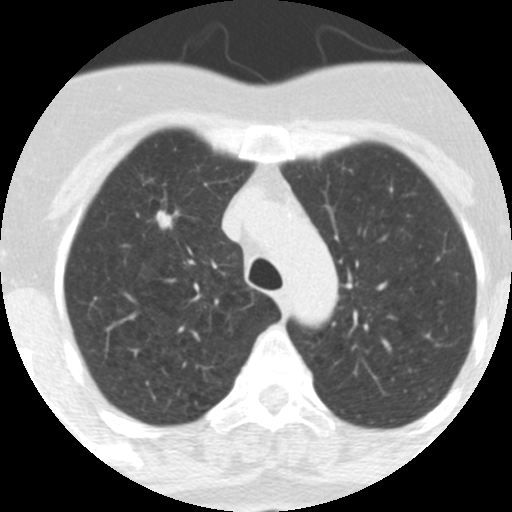
Low-dose screening chest CT, one axial slice; position 242 of 313 along the scan axis; reconstruction kernel STANDARD; lung window (W 1500 / L -600 HU); 2.5 mm slice thickness; 512 × 512 image matrix, field of view 253 × 253 mm.
Annotated regions visible in this slice (manually delineated by an expert):
- lesion 1 (tumor, upper lobe of right lung): bounding box (x1, y1, x2, y2) in pixels: (156, 210, 179, 229)